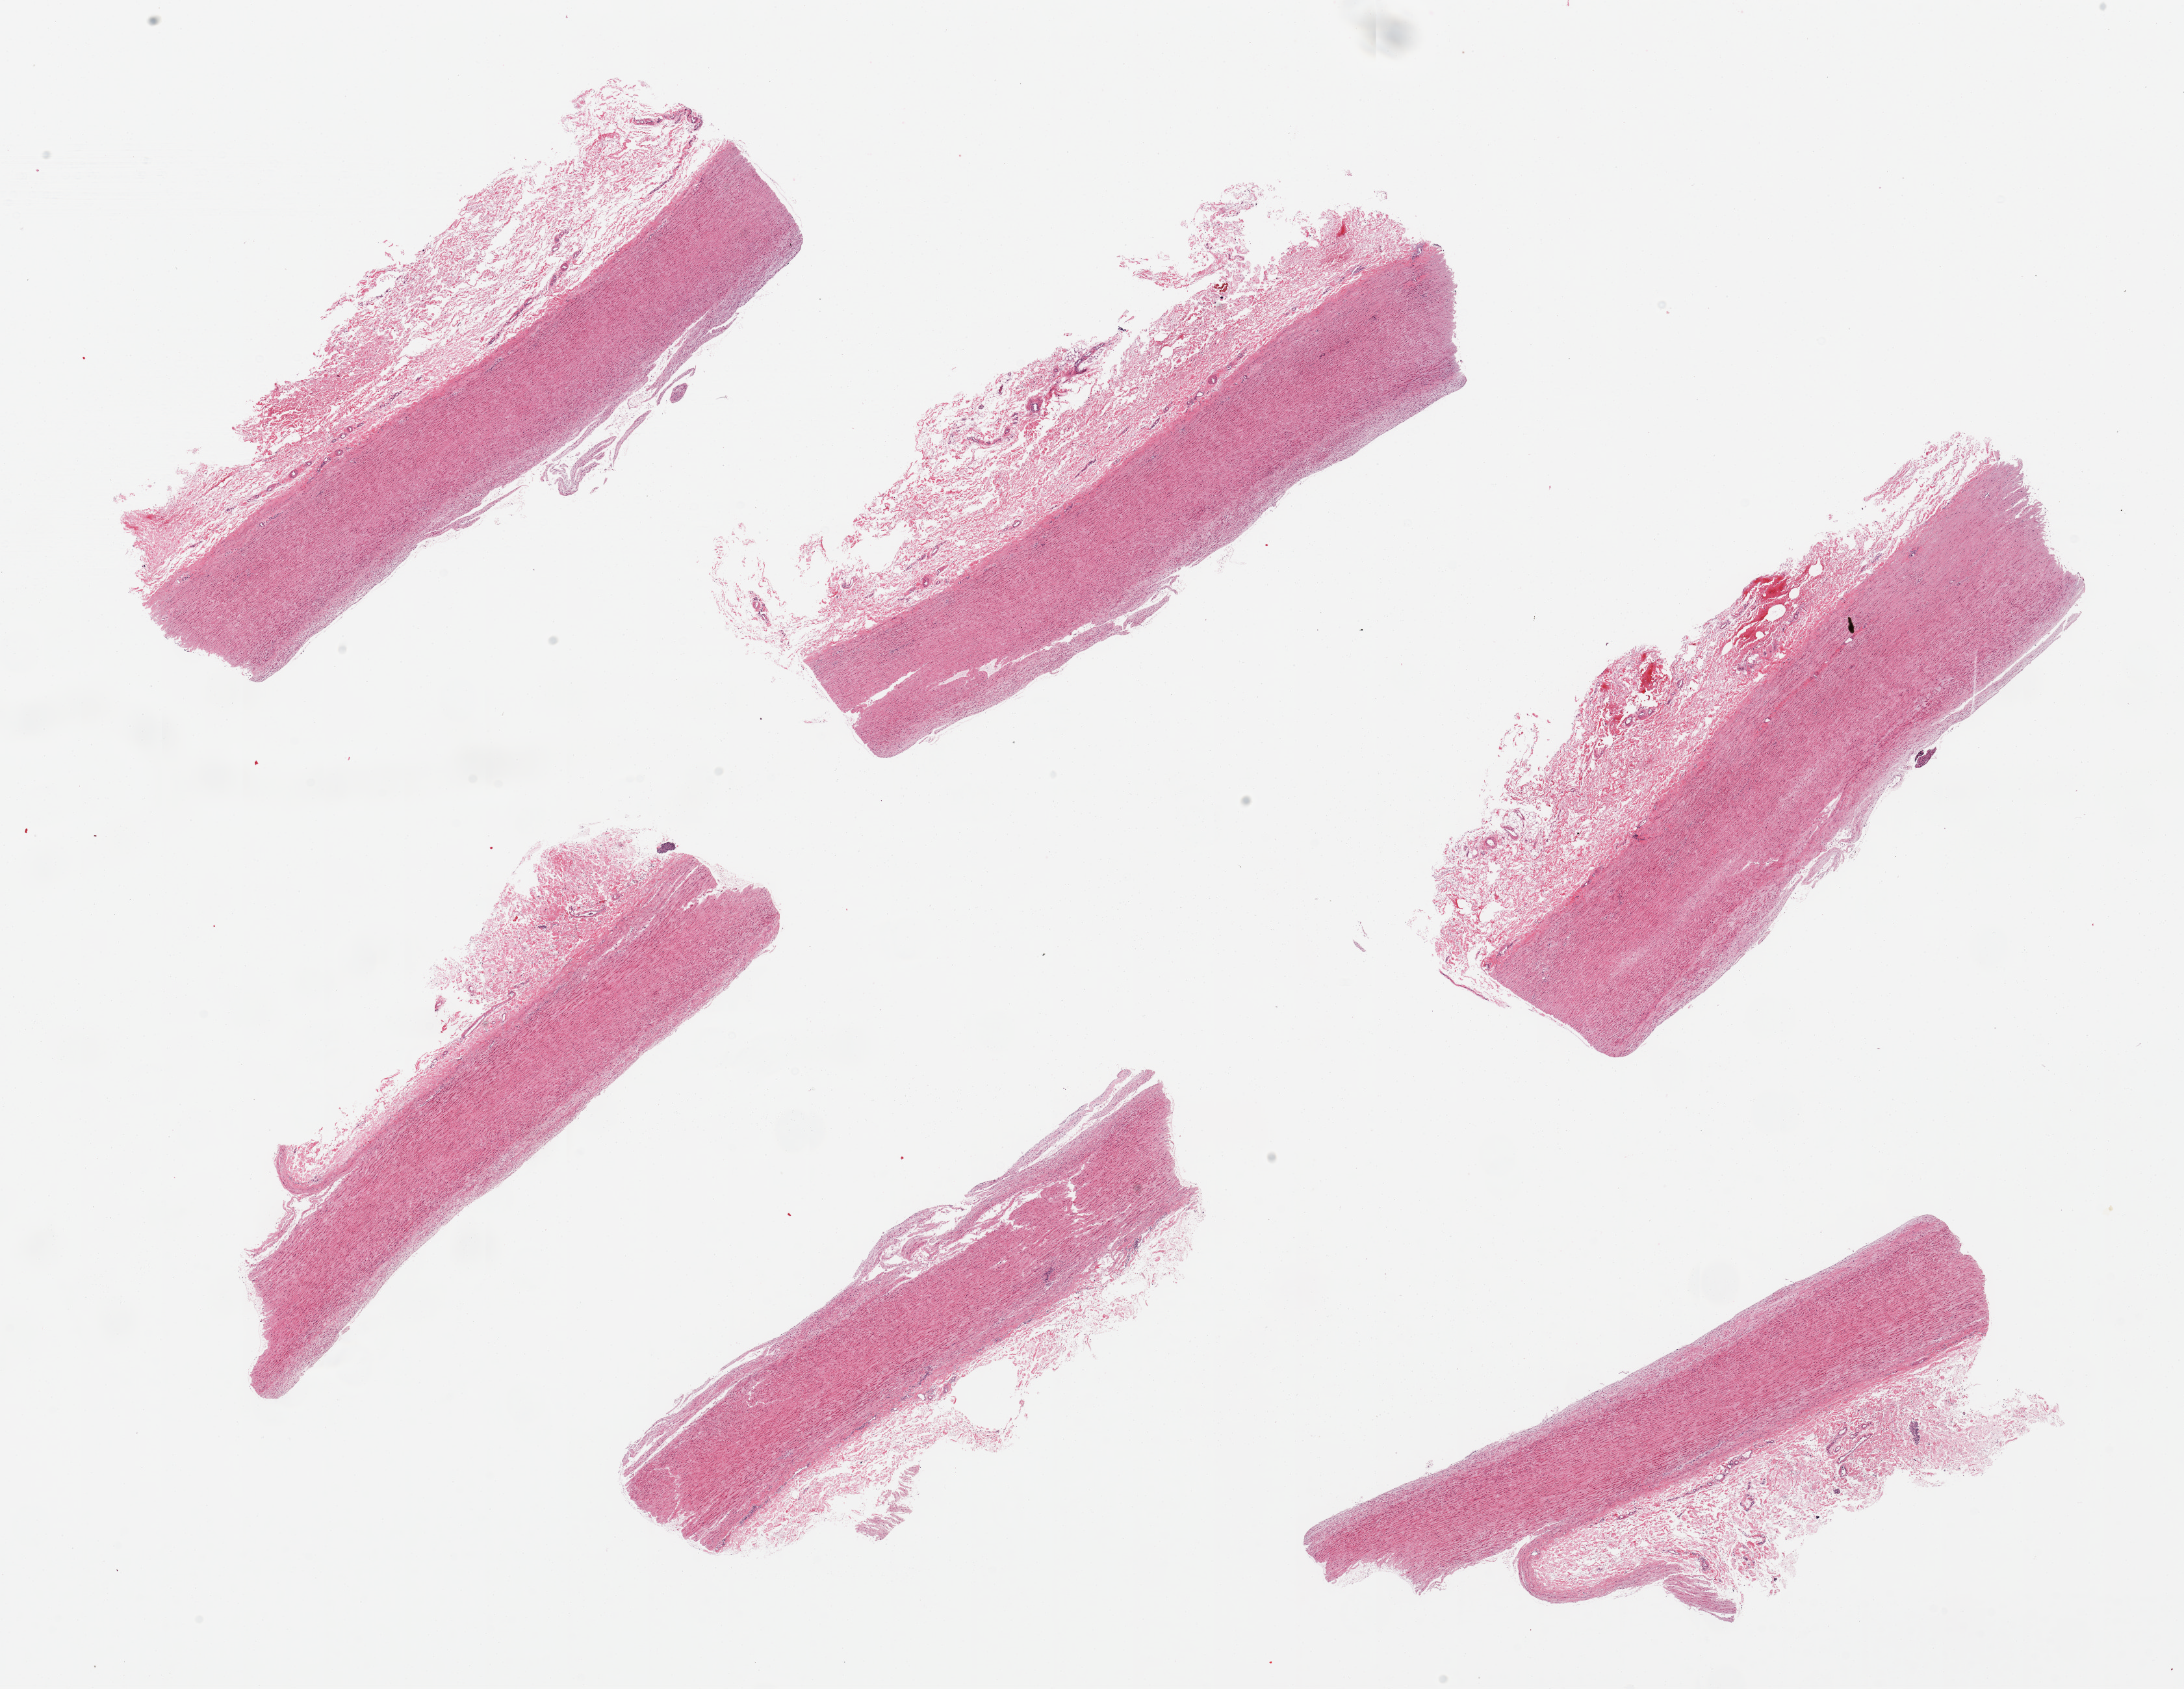
Whole-slide image, hematoxylin and eosin (H&E) stain, brightfield, whole scanned area (about 26.6 x 20.6 mm, acquisition: 20x scan) shown as a low-resolution overview, PAXgene-fixed paraffin-embedded (PFPE) section, target tissue: aorta, tissue donor sample. Male donor.
• reviewer comment on this tissue sample: 6 pieces; early plaque formation; all have up to 1.5mm attached adventitial fat